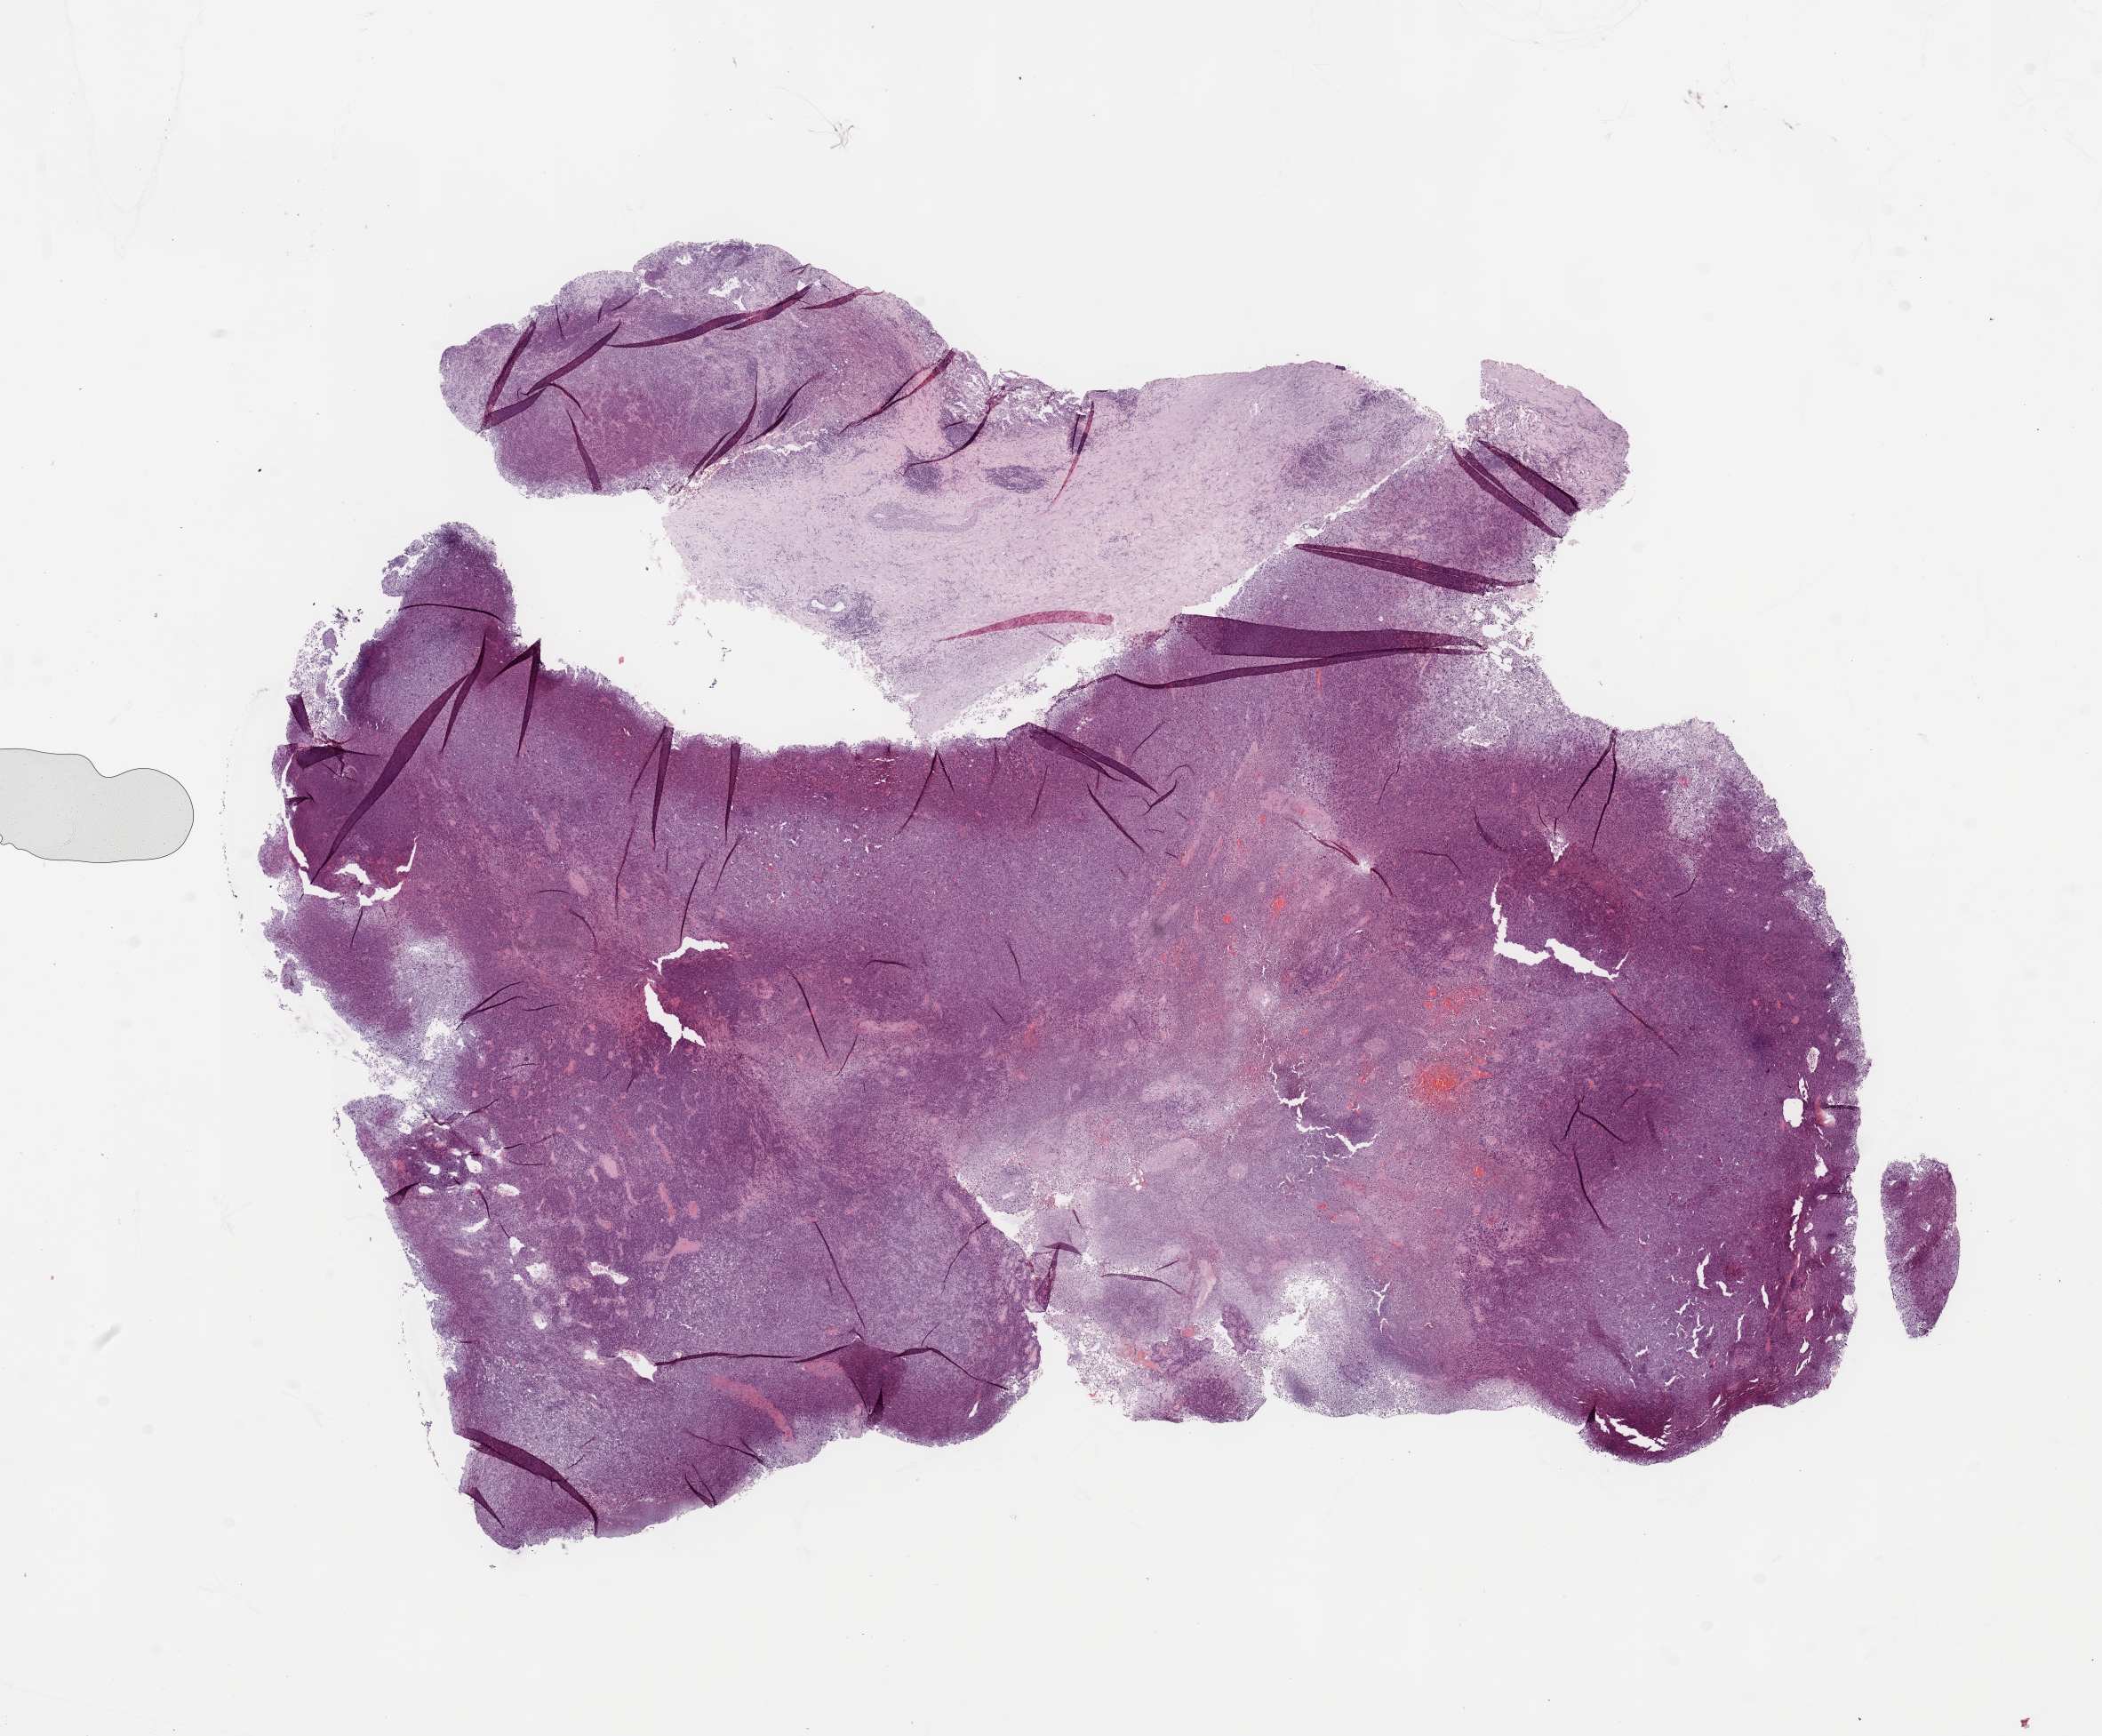
H&E-stained whole-slide image, low-resolution overview of the scanned area, about 18.7 x 15.4 mm (from a 20x scan). Tumour tissue sample, lung. Patient: female, age 70 years. Histologic grade: G3 (poorly differentiated).
Primary tumour site (as recorded): right lower lobe. Histologic diagnosis: Squamous cell carcinoma, NOS.